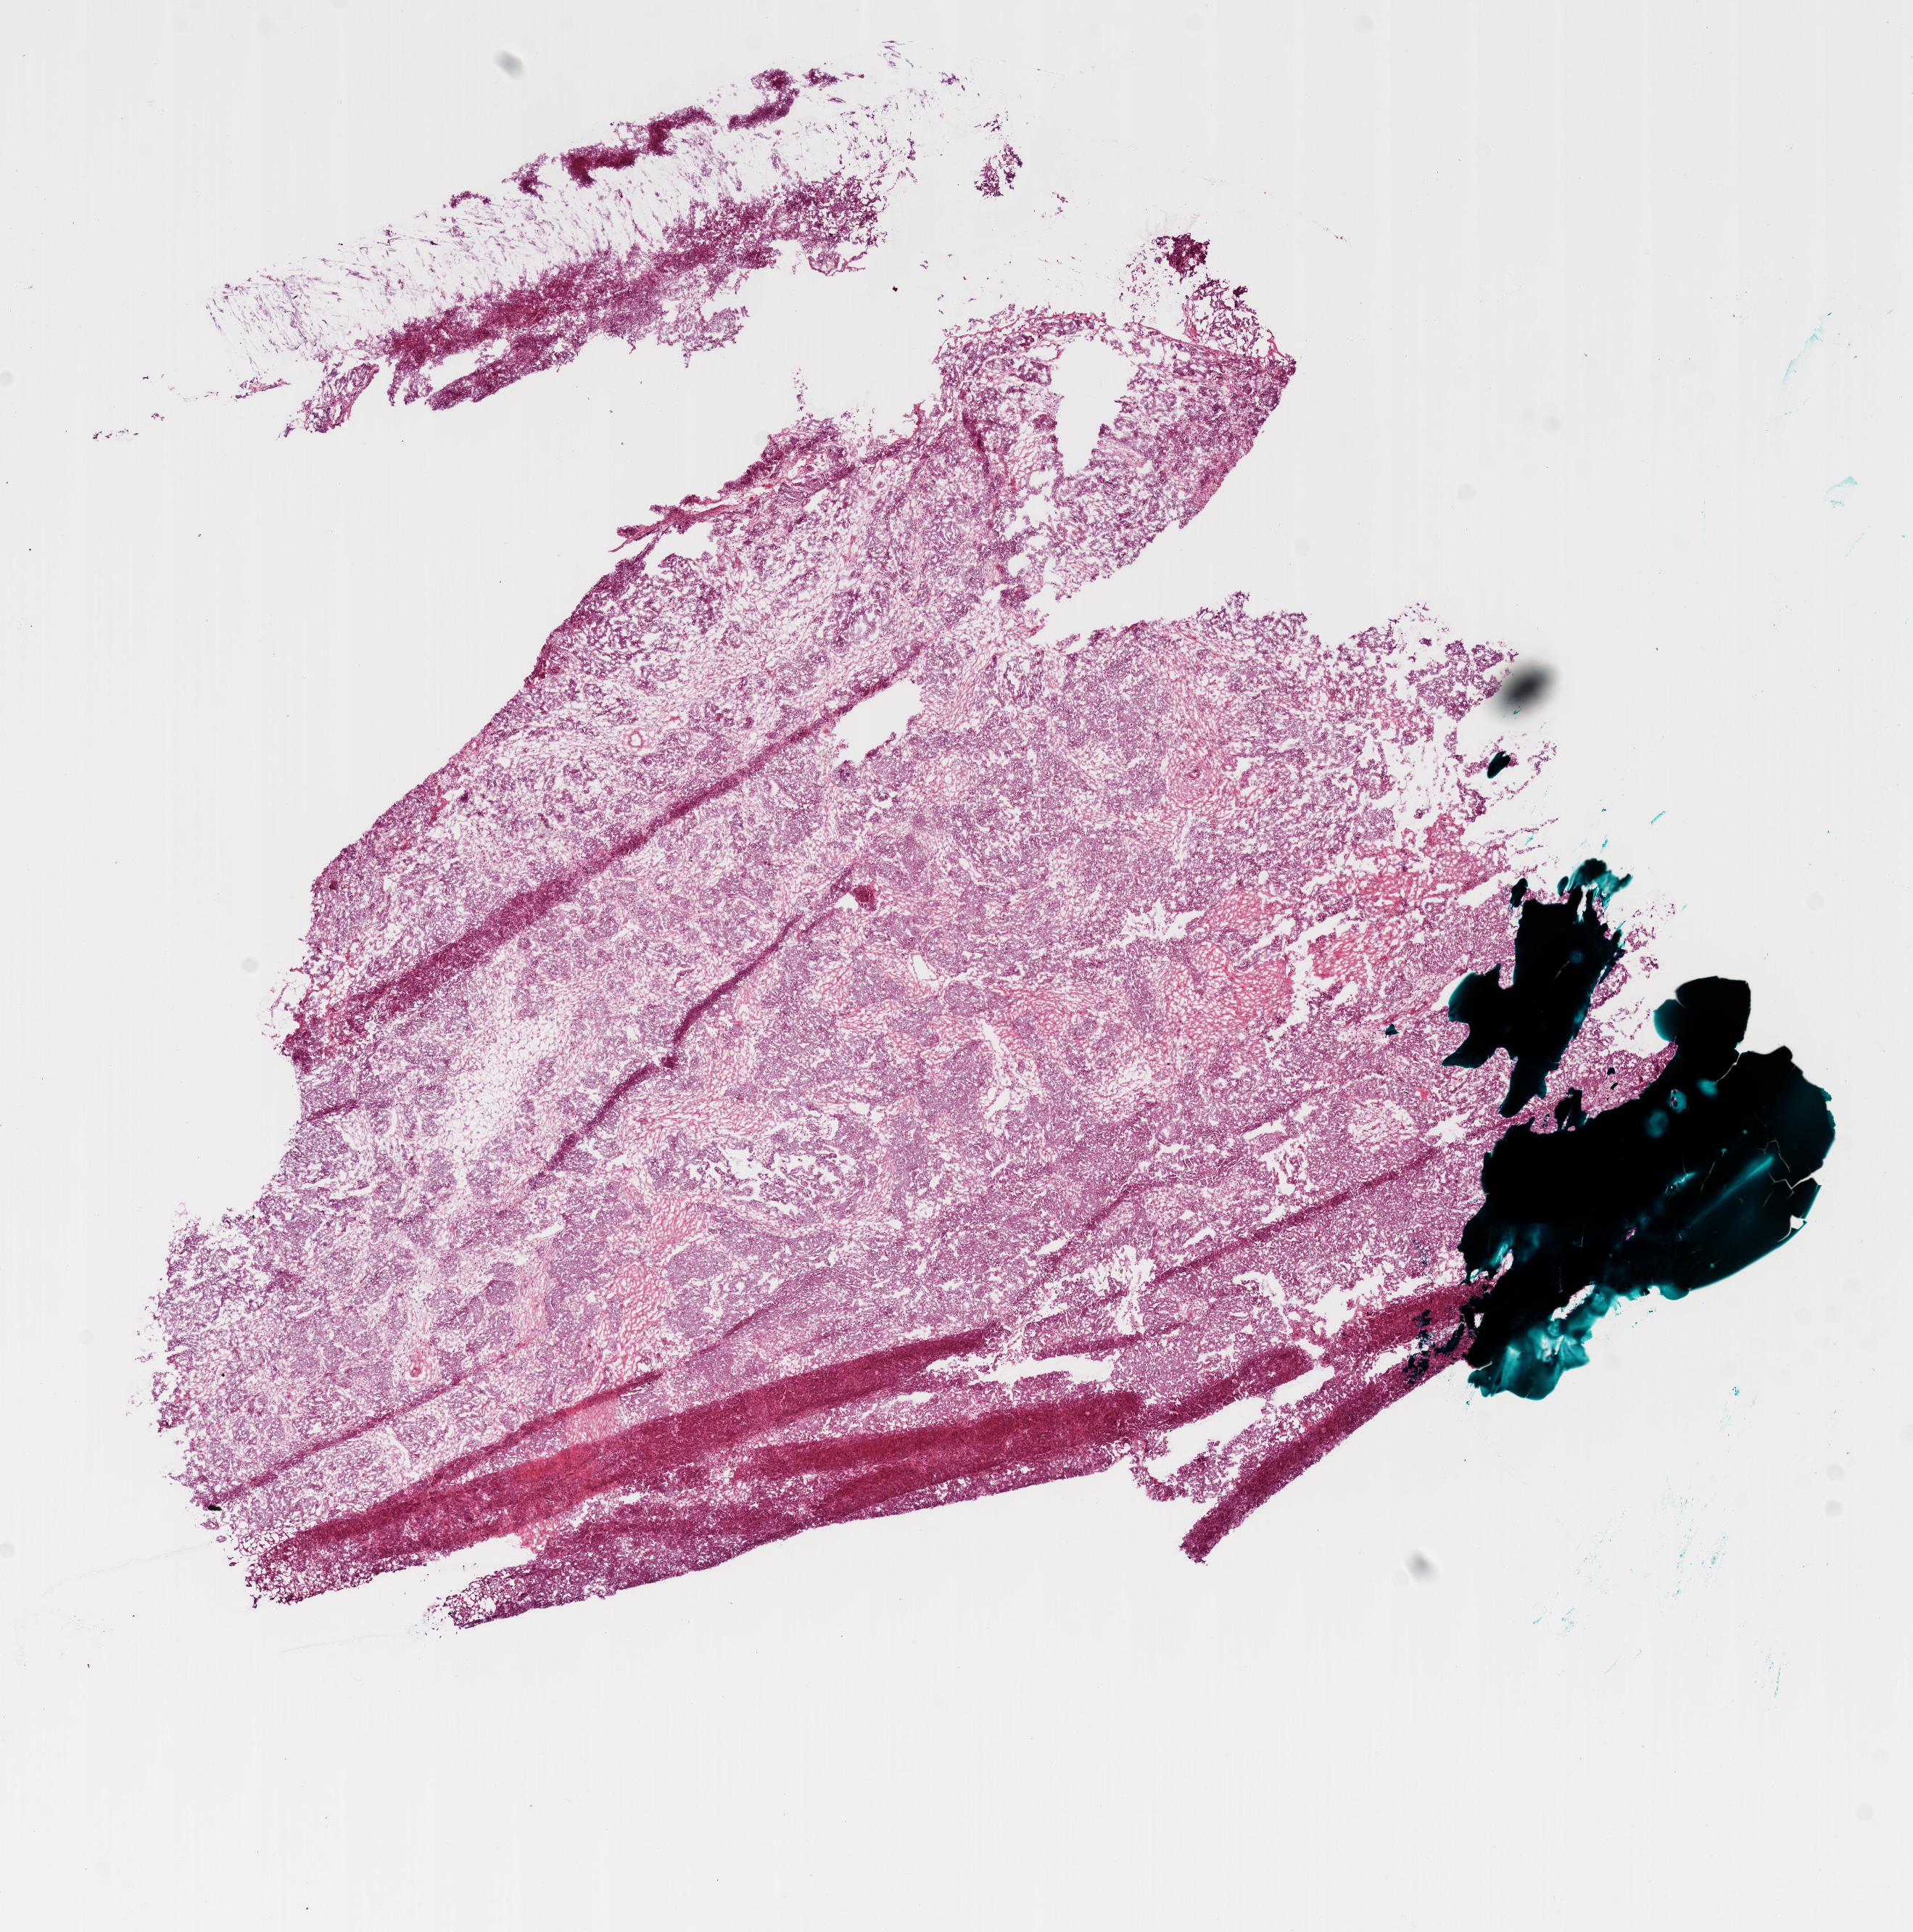
H&E-stained whole-slide image, low-resolution overview of the scanned area, about 10.6 x 10.7 mm, frozen section, primary tumour sample from the ovary. Female, age 48 years at initial diagnosis. Histologic grade: G3 (poorly differentiated). Pathologist review of this section (percent, as recorded): tumour cells 90%, tumour nuclei 95%, normal cells 5%, stromal cells 5%, necrosis 0%.
Diagnosis: Serous cystadenocarcinoma, NOS. FIGO stage: IIIC.